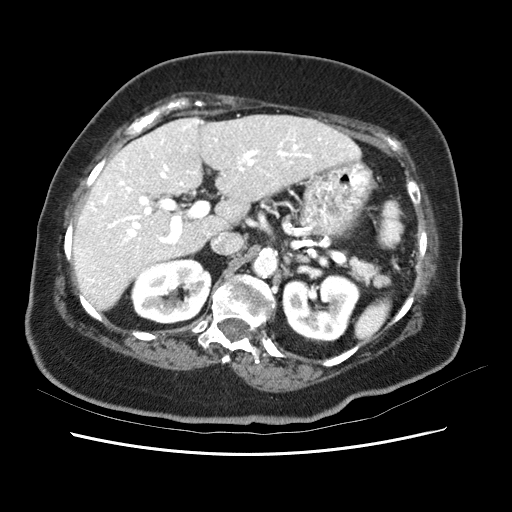
Contrast-enhanced abdominal CT (liver protocol), one axial slice; slice 34 of 62 in the series (ordered by position); reconstruction kernel STANDARD; 120 kVp; soft-tissue window (W 400 / L 40 HU); 2.5 mm slice thickness; 512 × 512 image matrix, field of view 340 × 340 mm. Case-level facts recorded for this patient, not image findings: diagnosis: hepatocellular carcinoma (patient treated with transarterial chemoembolisation; whether this scan precedes or follows treatment is not stated here); TNM stage (as recorded): Stage-I; Child-Pugh class: B; tumour size: 5.3 cm.
Structures marked on this image (semi-automatic segmentation, software-assisted and operator-edited):
- liver parenchyma outside the tumour (the mass and vessels are separate outlines, so this box may not span the whole liver): bounding box <74,114,362,308> (left, top, right, bottom; pixels)
- liver vessels: <81,123,348,295>